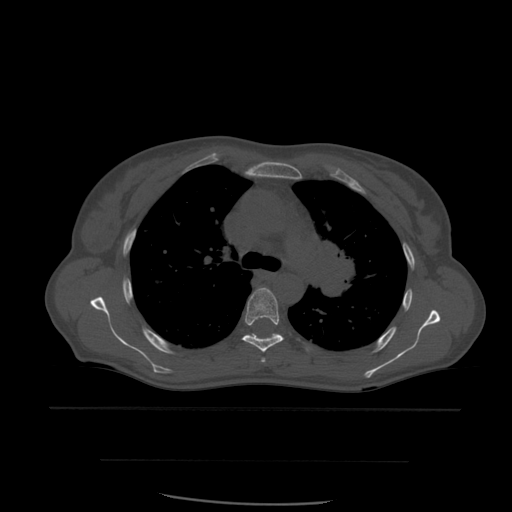
CT including the spine, one axial slice. Slice 410 of 574 in the series (ordered by position). Bone window (W 1800 / L 400 HU). 1.25 mm slice thickness. 512 × 512 image matrix. Patient age 48 years. From the clinical record (not read from this slice): primary cancer: lung; vertebrae with lytic lesions (as recorded): T11.
Outlined on this slice (semi-automatic segmentation, software-assisted and operator-edited):
- T4 vertebra: box from (x=261, y=358) to (x=266, y=363) px
- T5 vertebra: (x=242, y=288)–(x=284, y=353)
- T6 vertebra: (x=249, y=334)–(x=277, y=339)